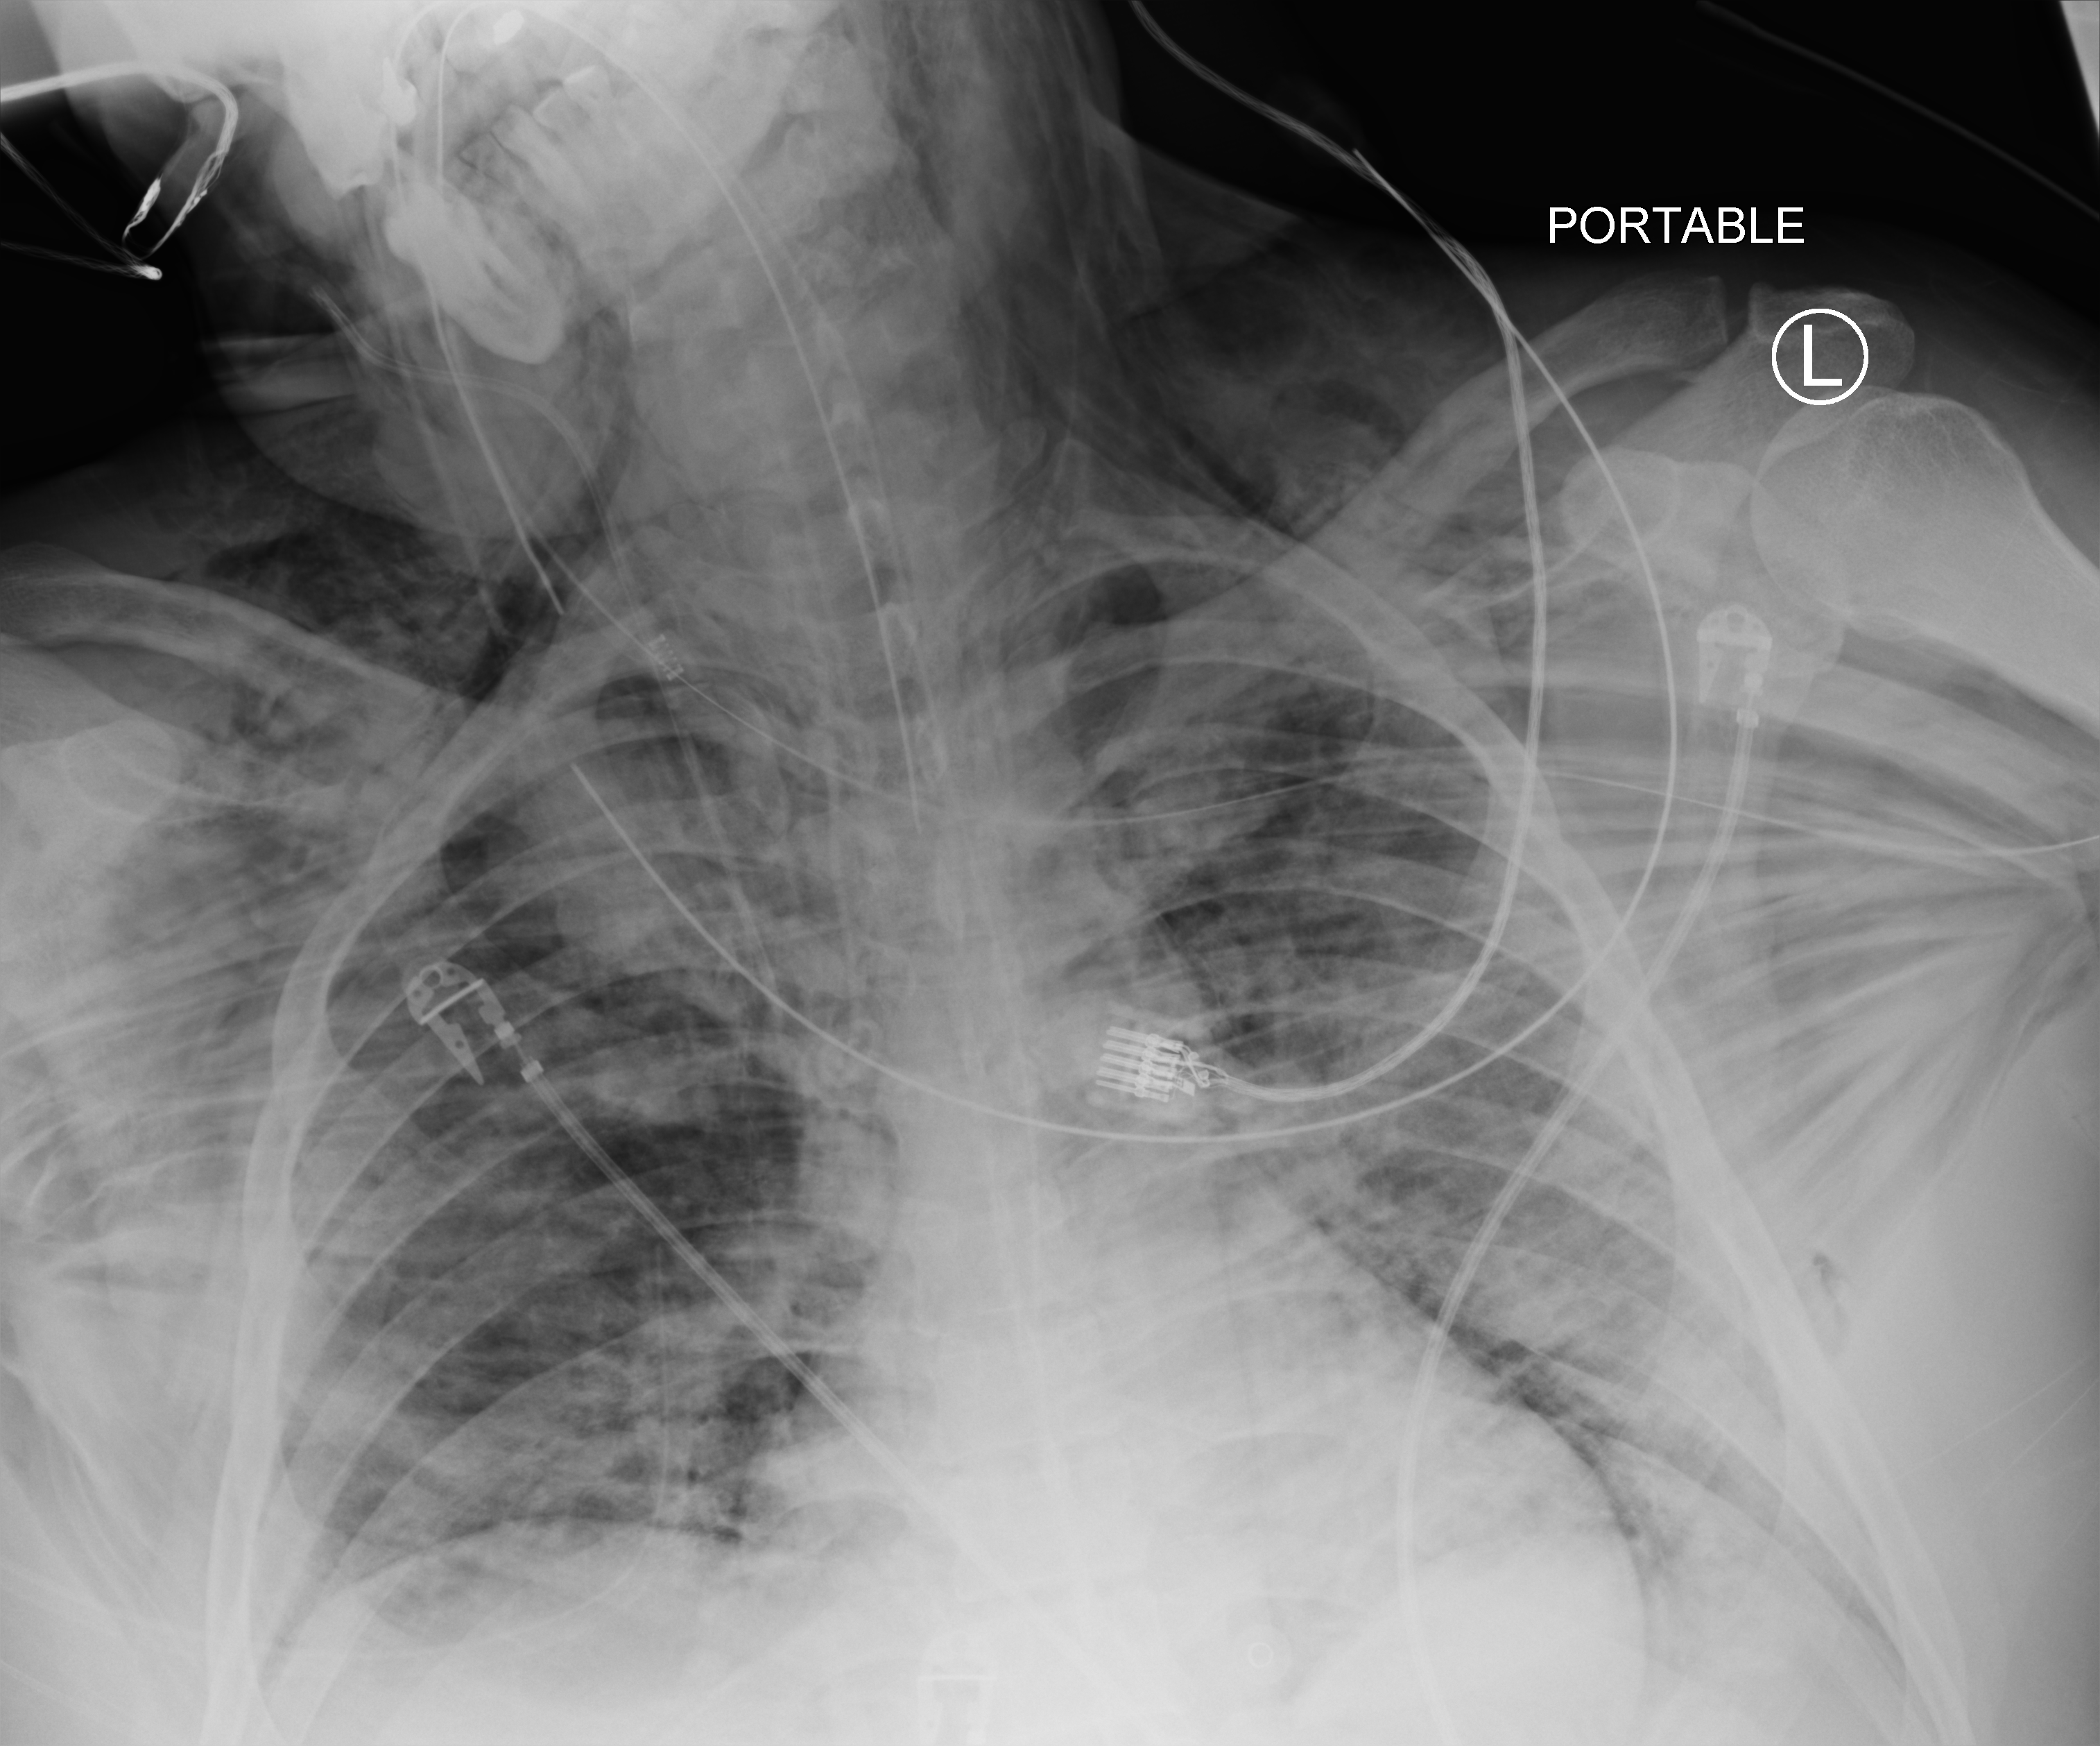
Portable chest radiograph, anteroposterior (AP) projection. Patient hospitalised with COVID-19; male, aged 18–59 years.
Hospital-stay facts (about this admission, not read from this image; timing relative to this image not recorded): mechanically ventilated during this hospital stay: yes; length of hospital stay: 29 days.